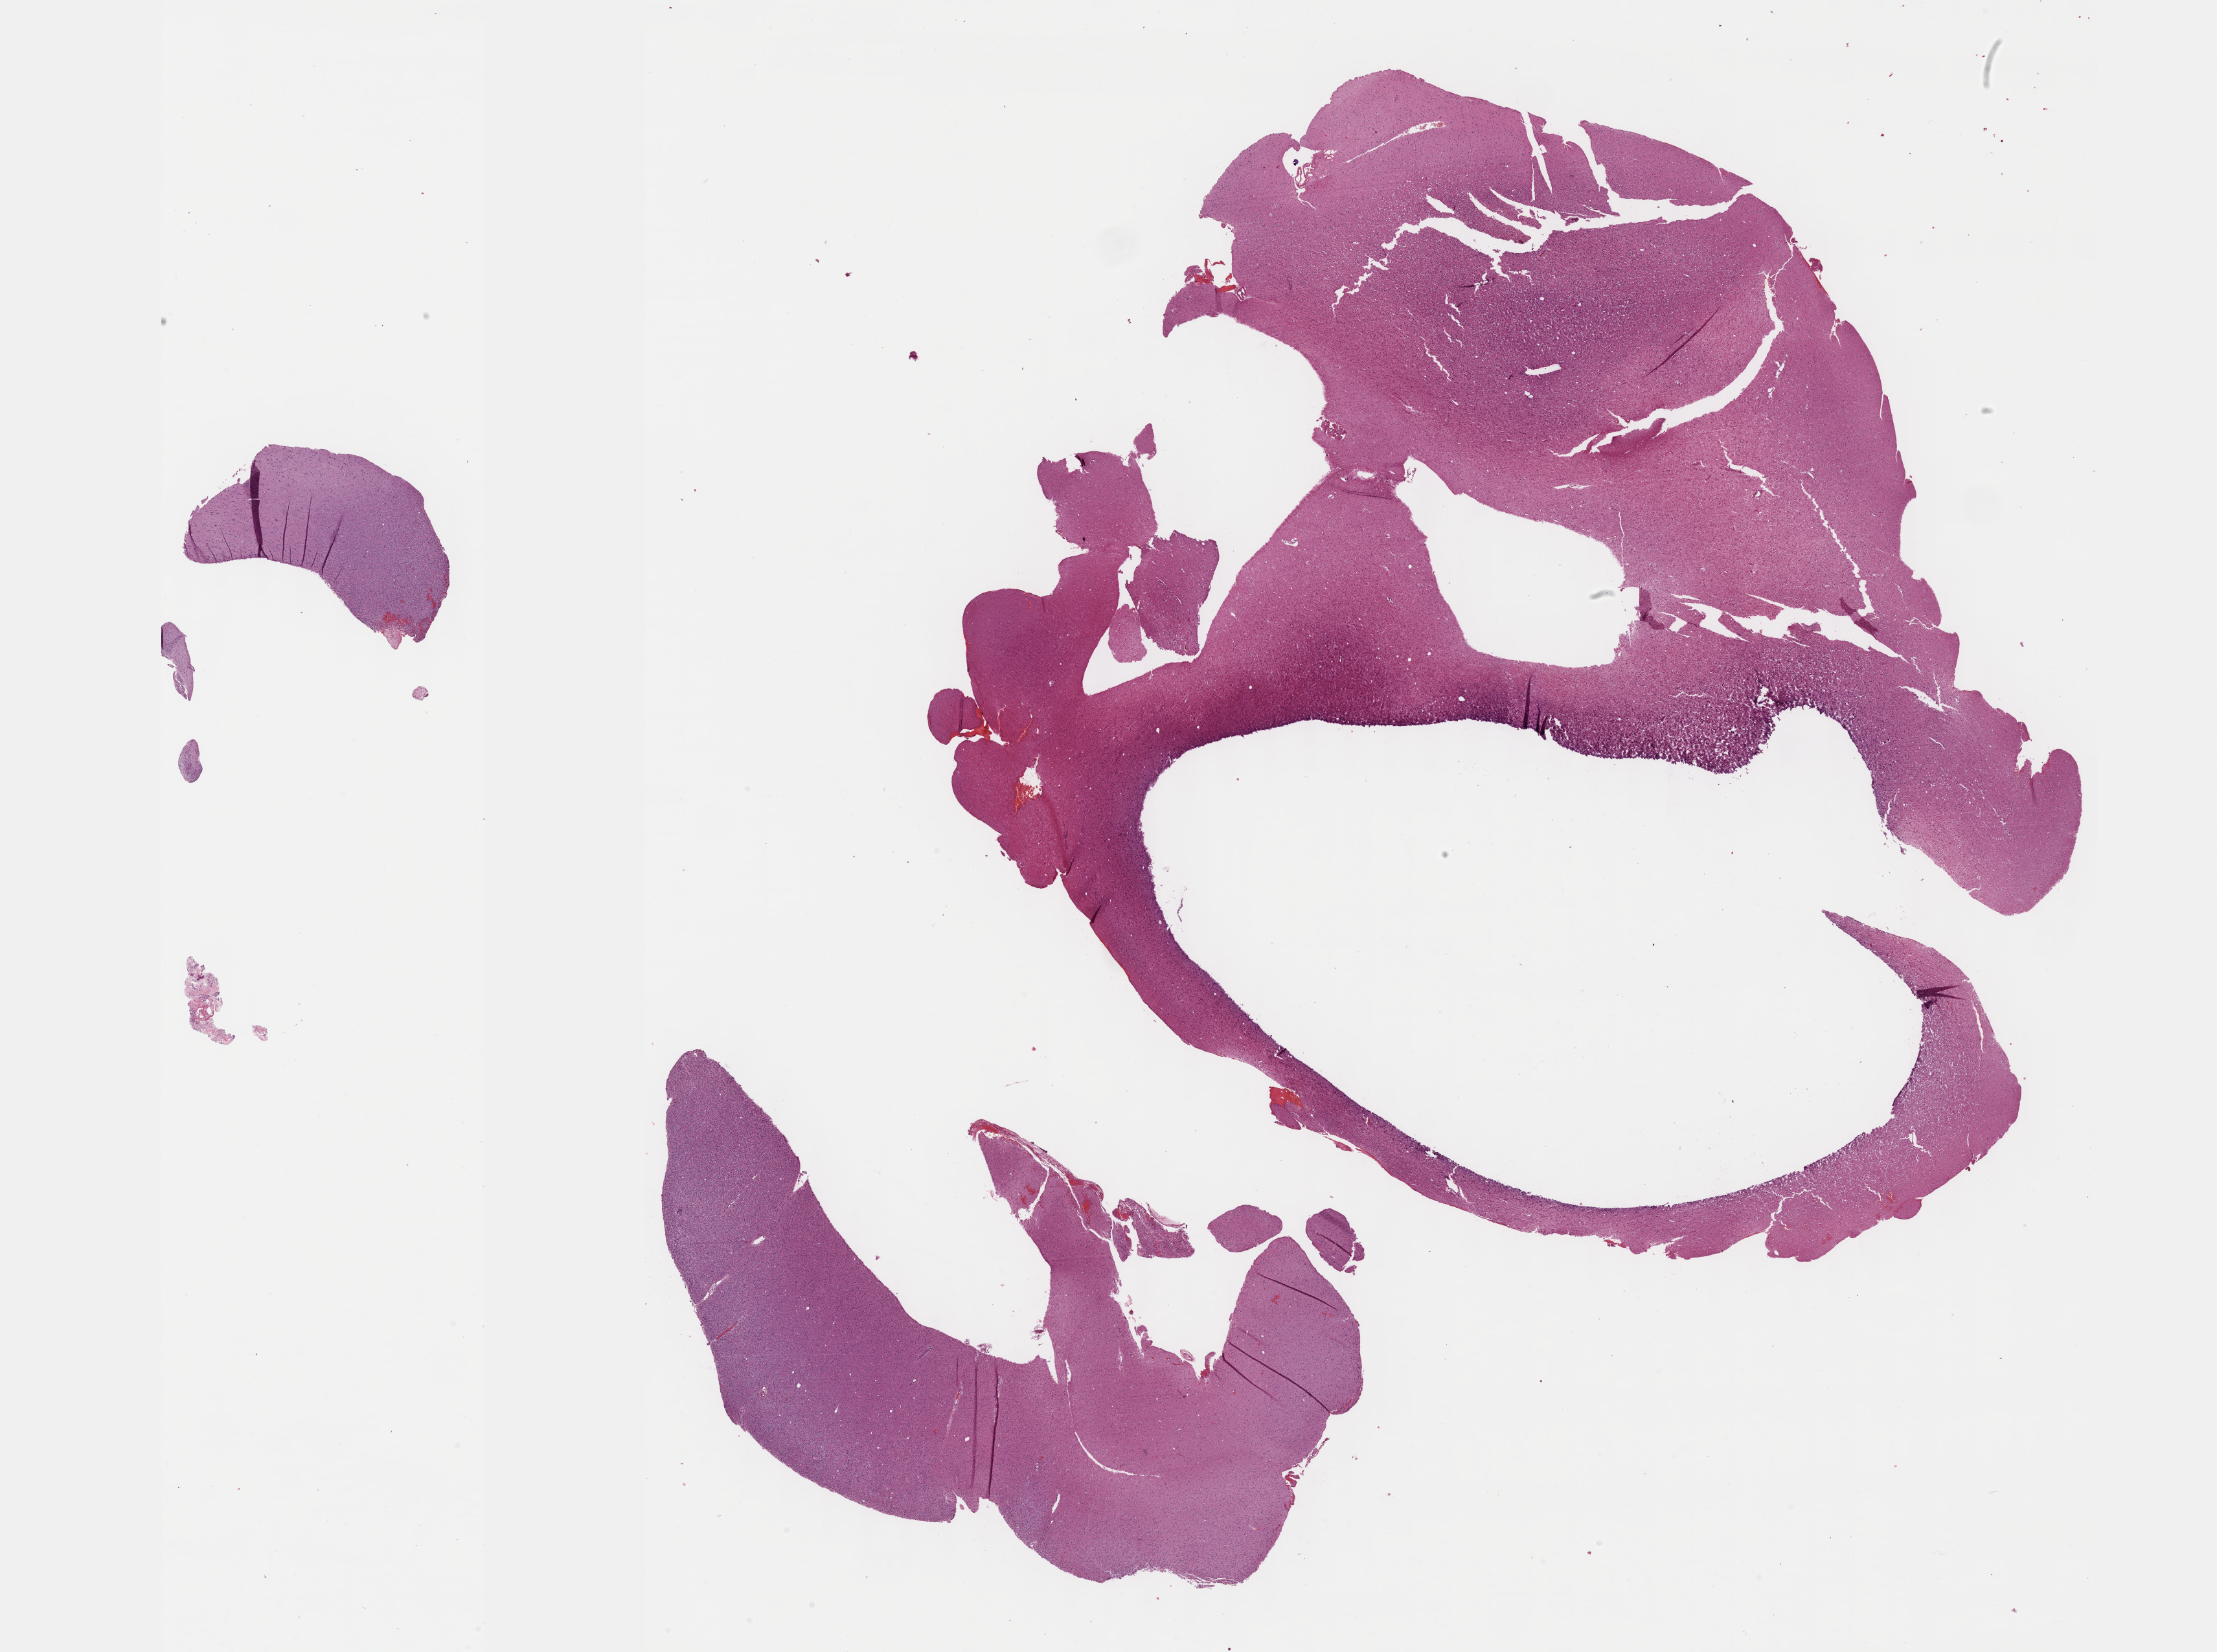
H&E-stained whole-slide image, a low-resolution overview of the entire scanned area, about 27.7 x 20.6 mm (acquisition: 40x scan), formalin-fixed paraffin-embedded (FFPE) diagnostic section, sample: primary tumour, brain. Patient: female, age at initial diagnosis 29 years.
Diagnosis: Oligodendroglioma, NOS (cerebrum).